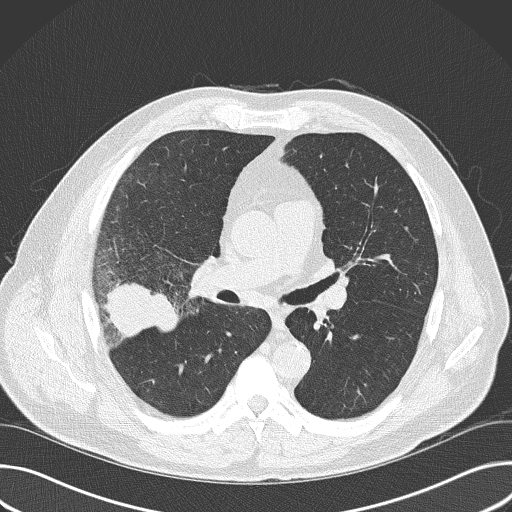
Chest CT (low-dose screening protocol), one axial image. First (baseline) screen. Lung window (W 1500 / L -600 HU). 120 kVp. Slice 95 of 157 in the series. Male participant, aged 56 years at enrolment.
Lesion marked by an expert reader, bounding box (x1, y1, x2, y2) in pixels: (80, 257, 183, 360). The exam's reader record, not a measurement of the box and not confirmed to be the same lesion: non-calcified nodule or mass ≥4 mm, right upper lobe, 6 × 5 mm, spiculated (stellate) margins, soft tissue attenuation. Official screen result: positive, change unspecified: nodule(s) >= 4 mm or enlarging nodule(s), mass(es), or other non-specific abnormalities suspicious for lung cancer. Participant outcome: lung cancer diagnosed 16 days after this screen — adenocarcinoma, NOS, right upper lobe, poorly differentiated (G3), stage IIB (AJCC 6th edition), 60 mm at pathology.